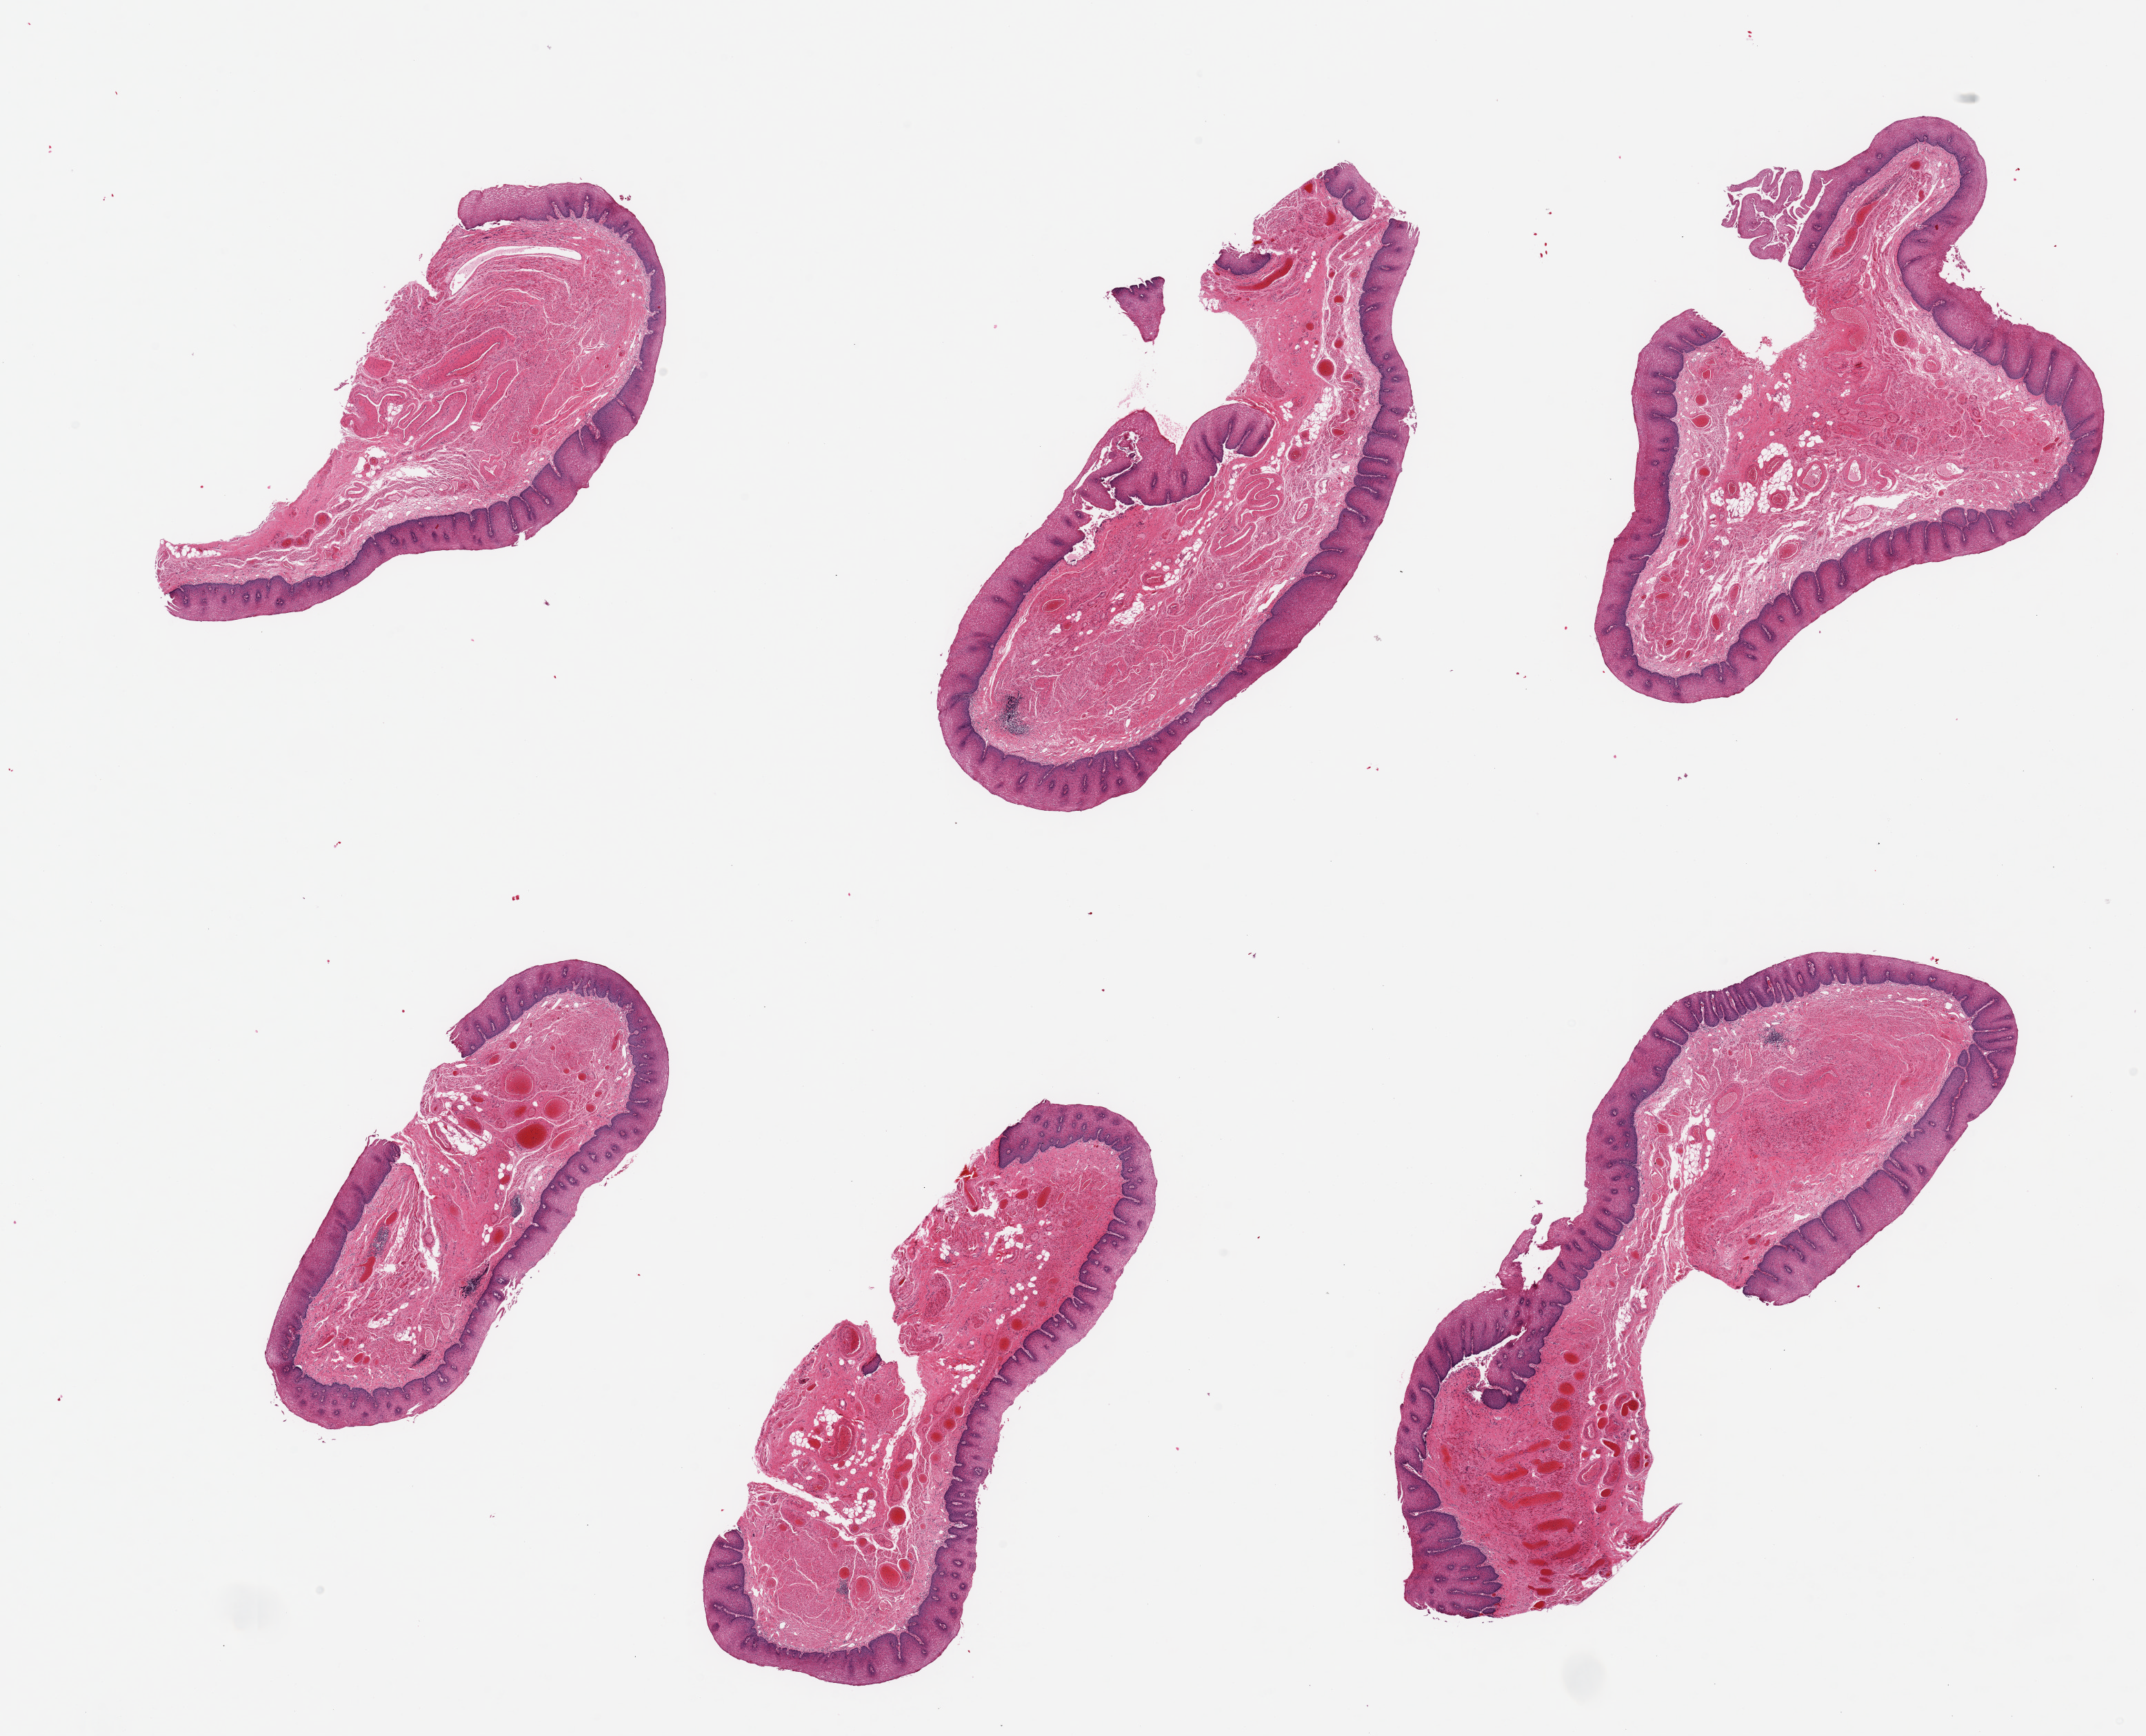
Haematoxylin and eosin whole-slide image — low-resolution overview of the scanned area, about 24.6 x 19.9 mm. PAXgene-fixed, paraffin-embedded tissue. Sampled site (target tissue): esophageal mucous membrane. Tissue donor sample. Donor sex: male.
Pathologist's review note for this sample: 6 pieces, squamous mucosa up to ~0.4mm, ~15-20% thickness.